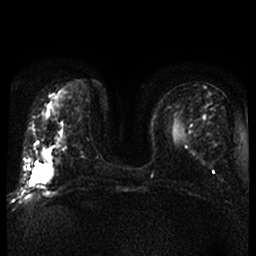
Breast MRI, one axial slice; slice 14 of 52 in the series (ordered by position); diffusion-weighted series; image 2 of 4 stored at this slice position (different b-values; order by instance number); 1.5 T; 4 mm slice thickness; 256 × 256 image matrix. Female patient.
Outlined on this slice (manually delineated by an expert):
- tumour on diffusion-weighted imaging: bounding box (x1, y1, x2, y2) in pixels: (32, 164, 53, 183)